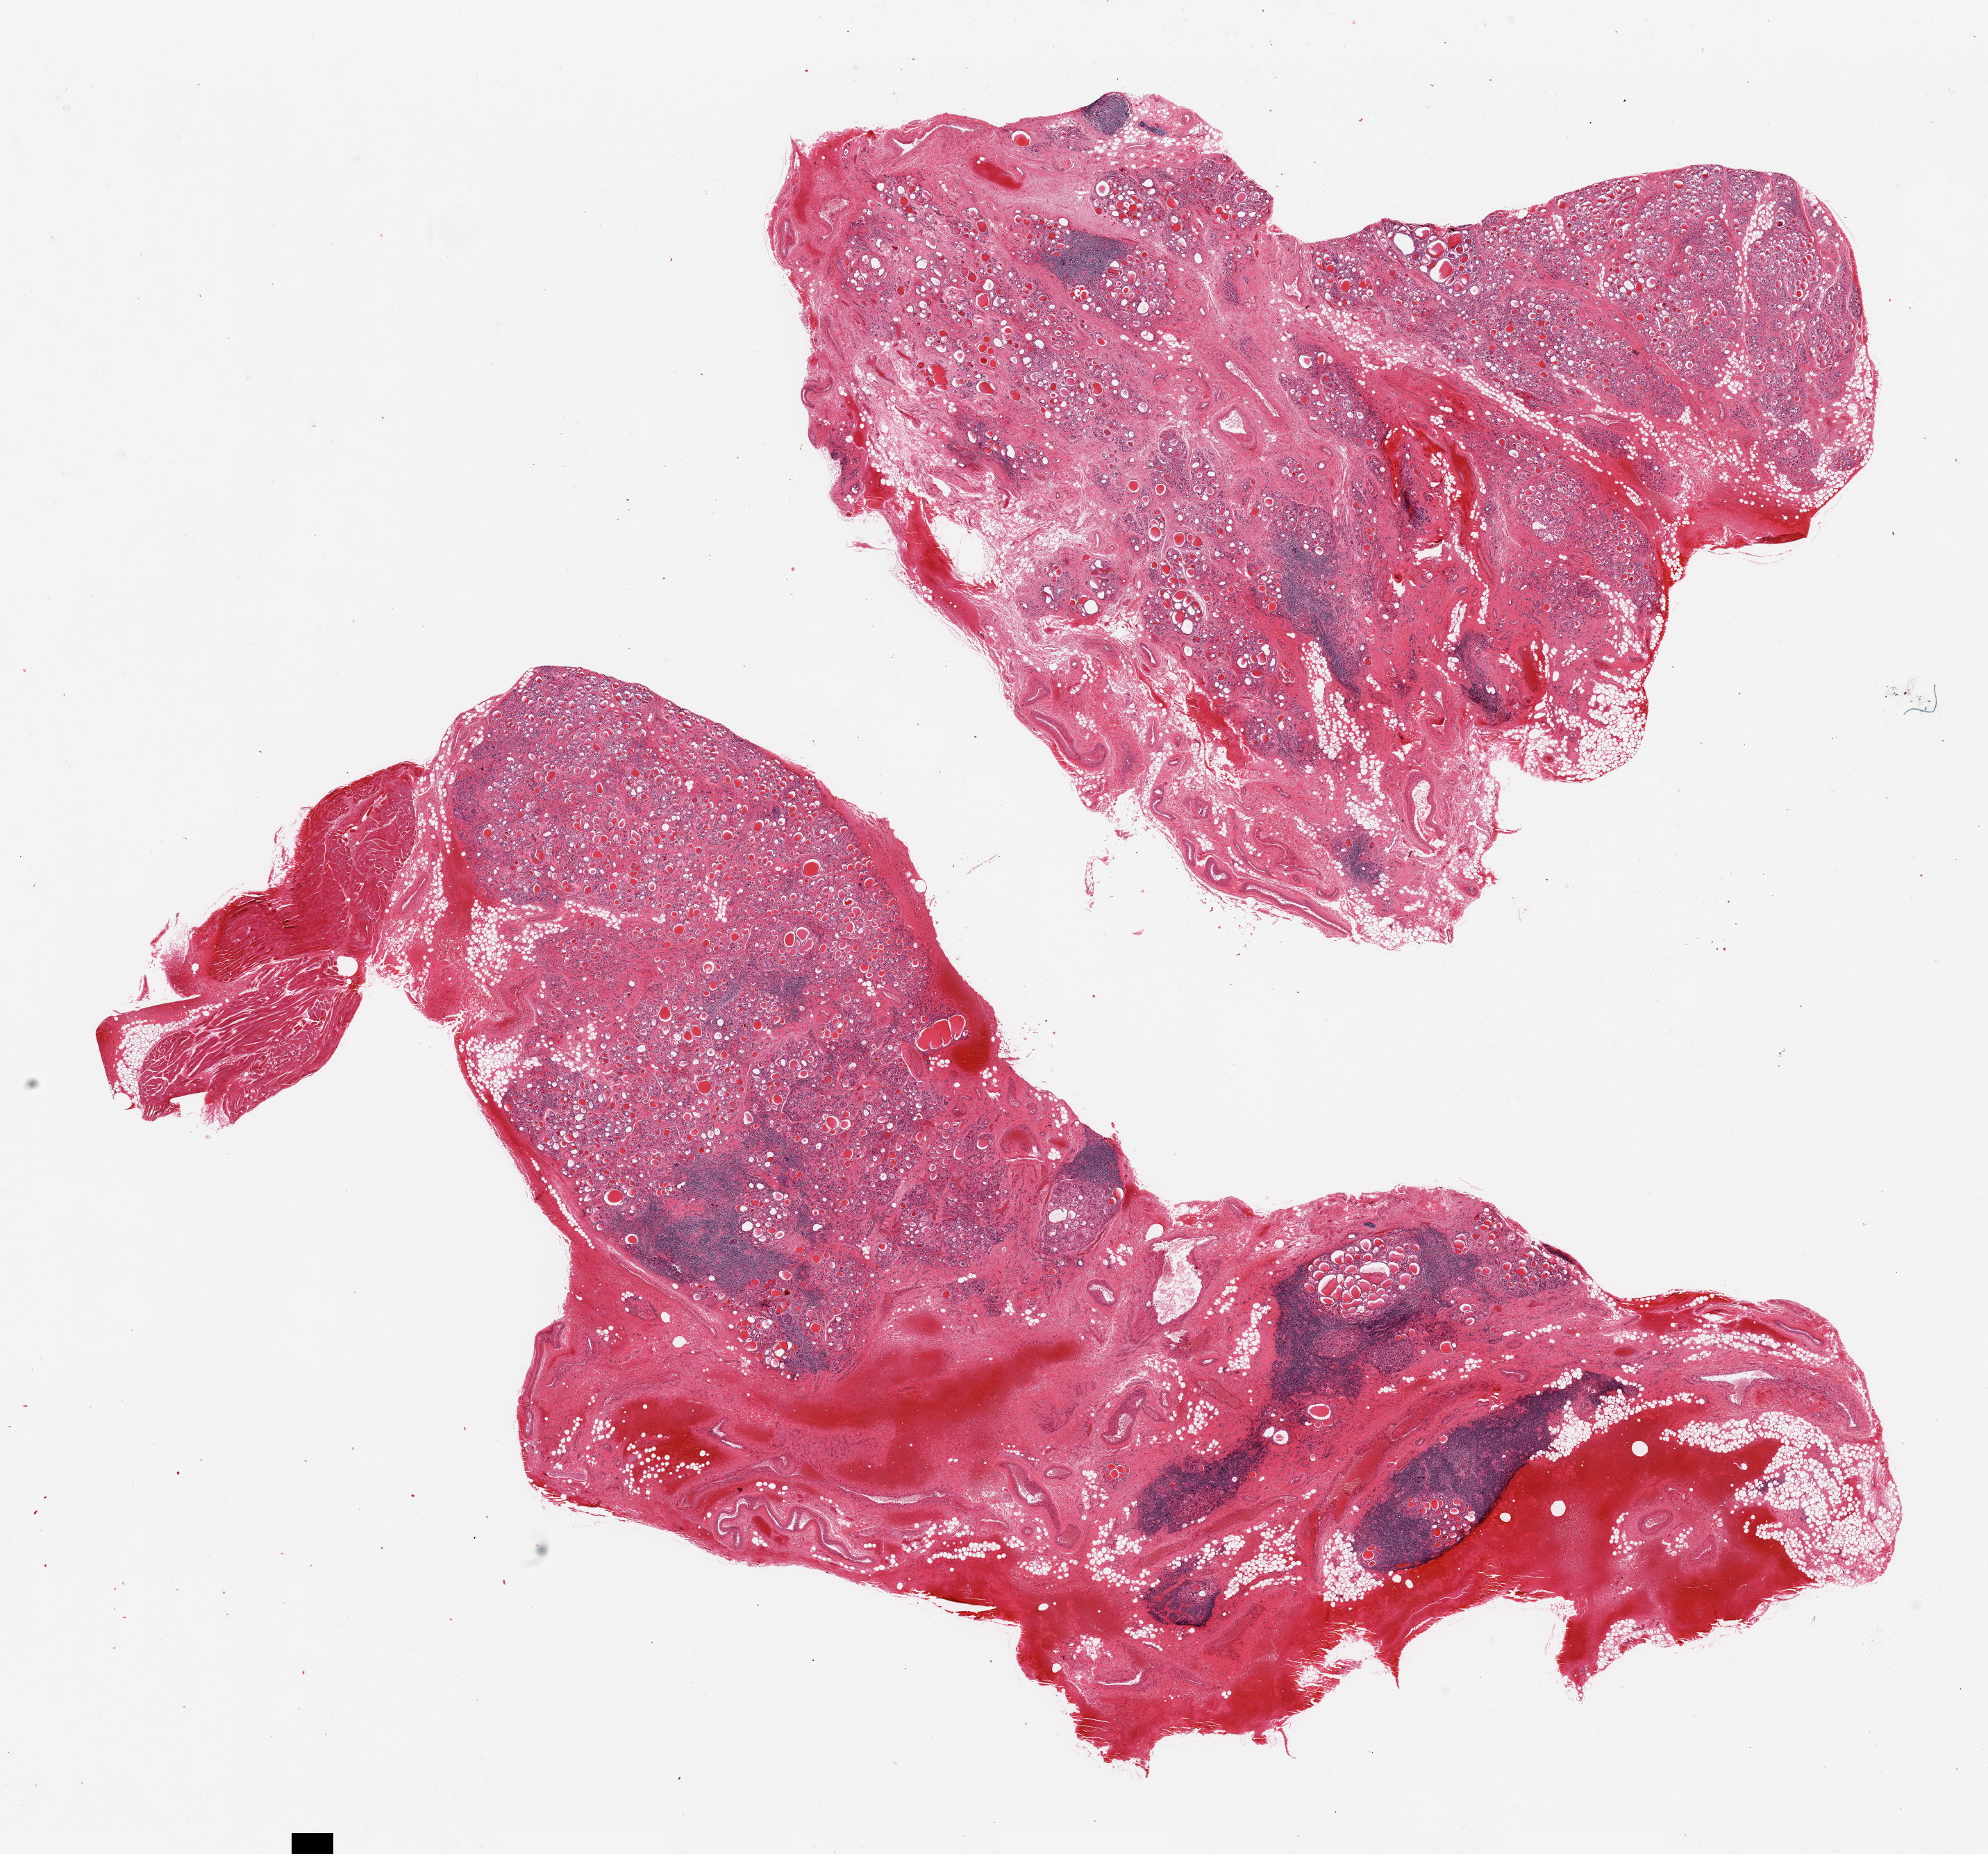
Whole-slide image, H&E stain, shown as a low-resolution overview of the whole scanned area (about 22.6 x 21.1 mm, acquisition: 20x scan); PAXgene-fixed paraffin-embedded (PFPE) section; section of thyroid (target tissue); tissue donor sample. Donor: female.
Reviewer comment on this tissue sample: 2 pieces; Hashimoto thyroiditis, moderate; 40% fibrovascular and adipose tissue.